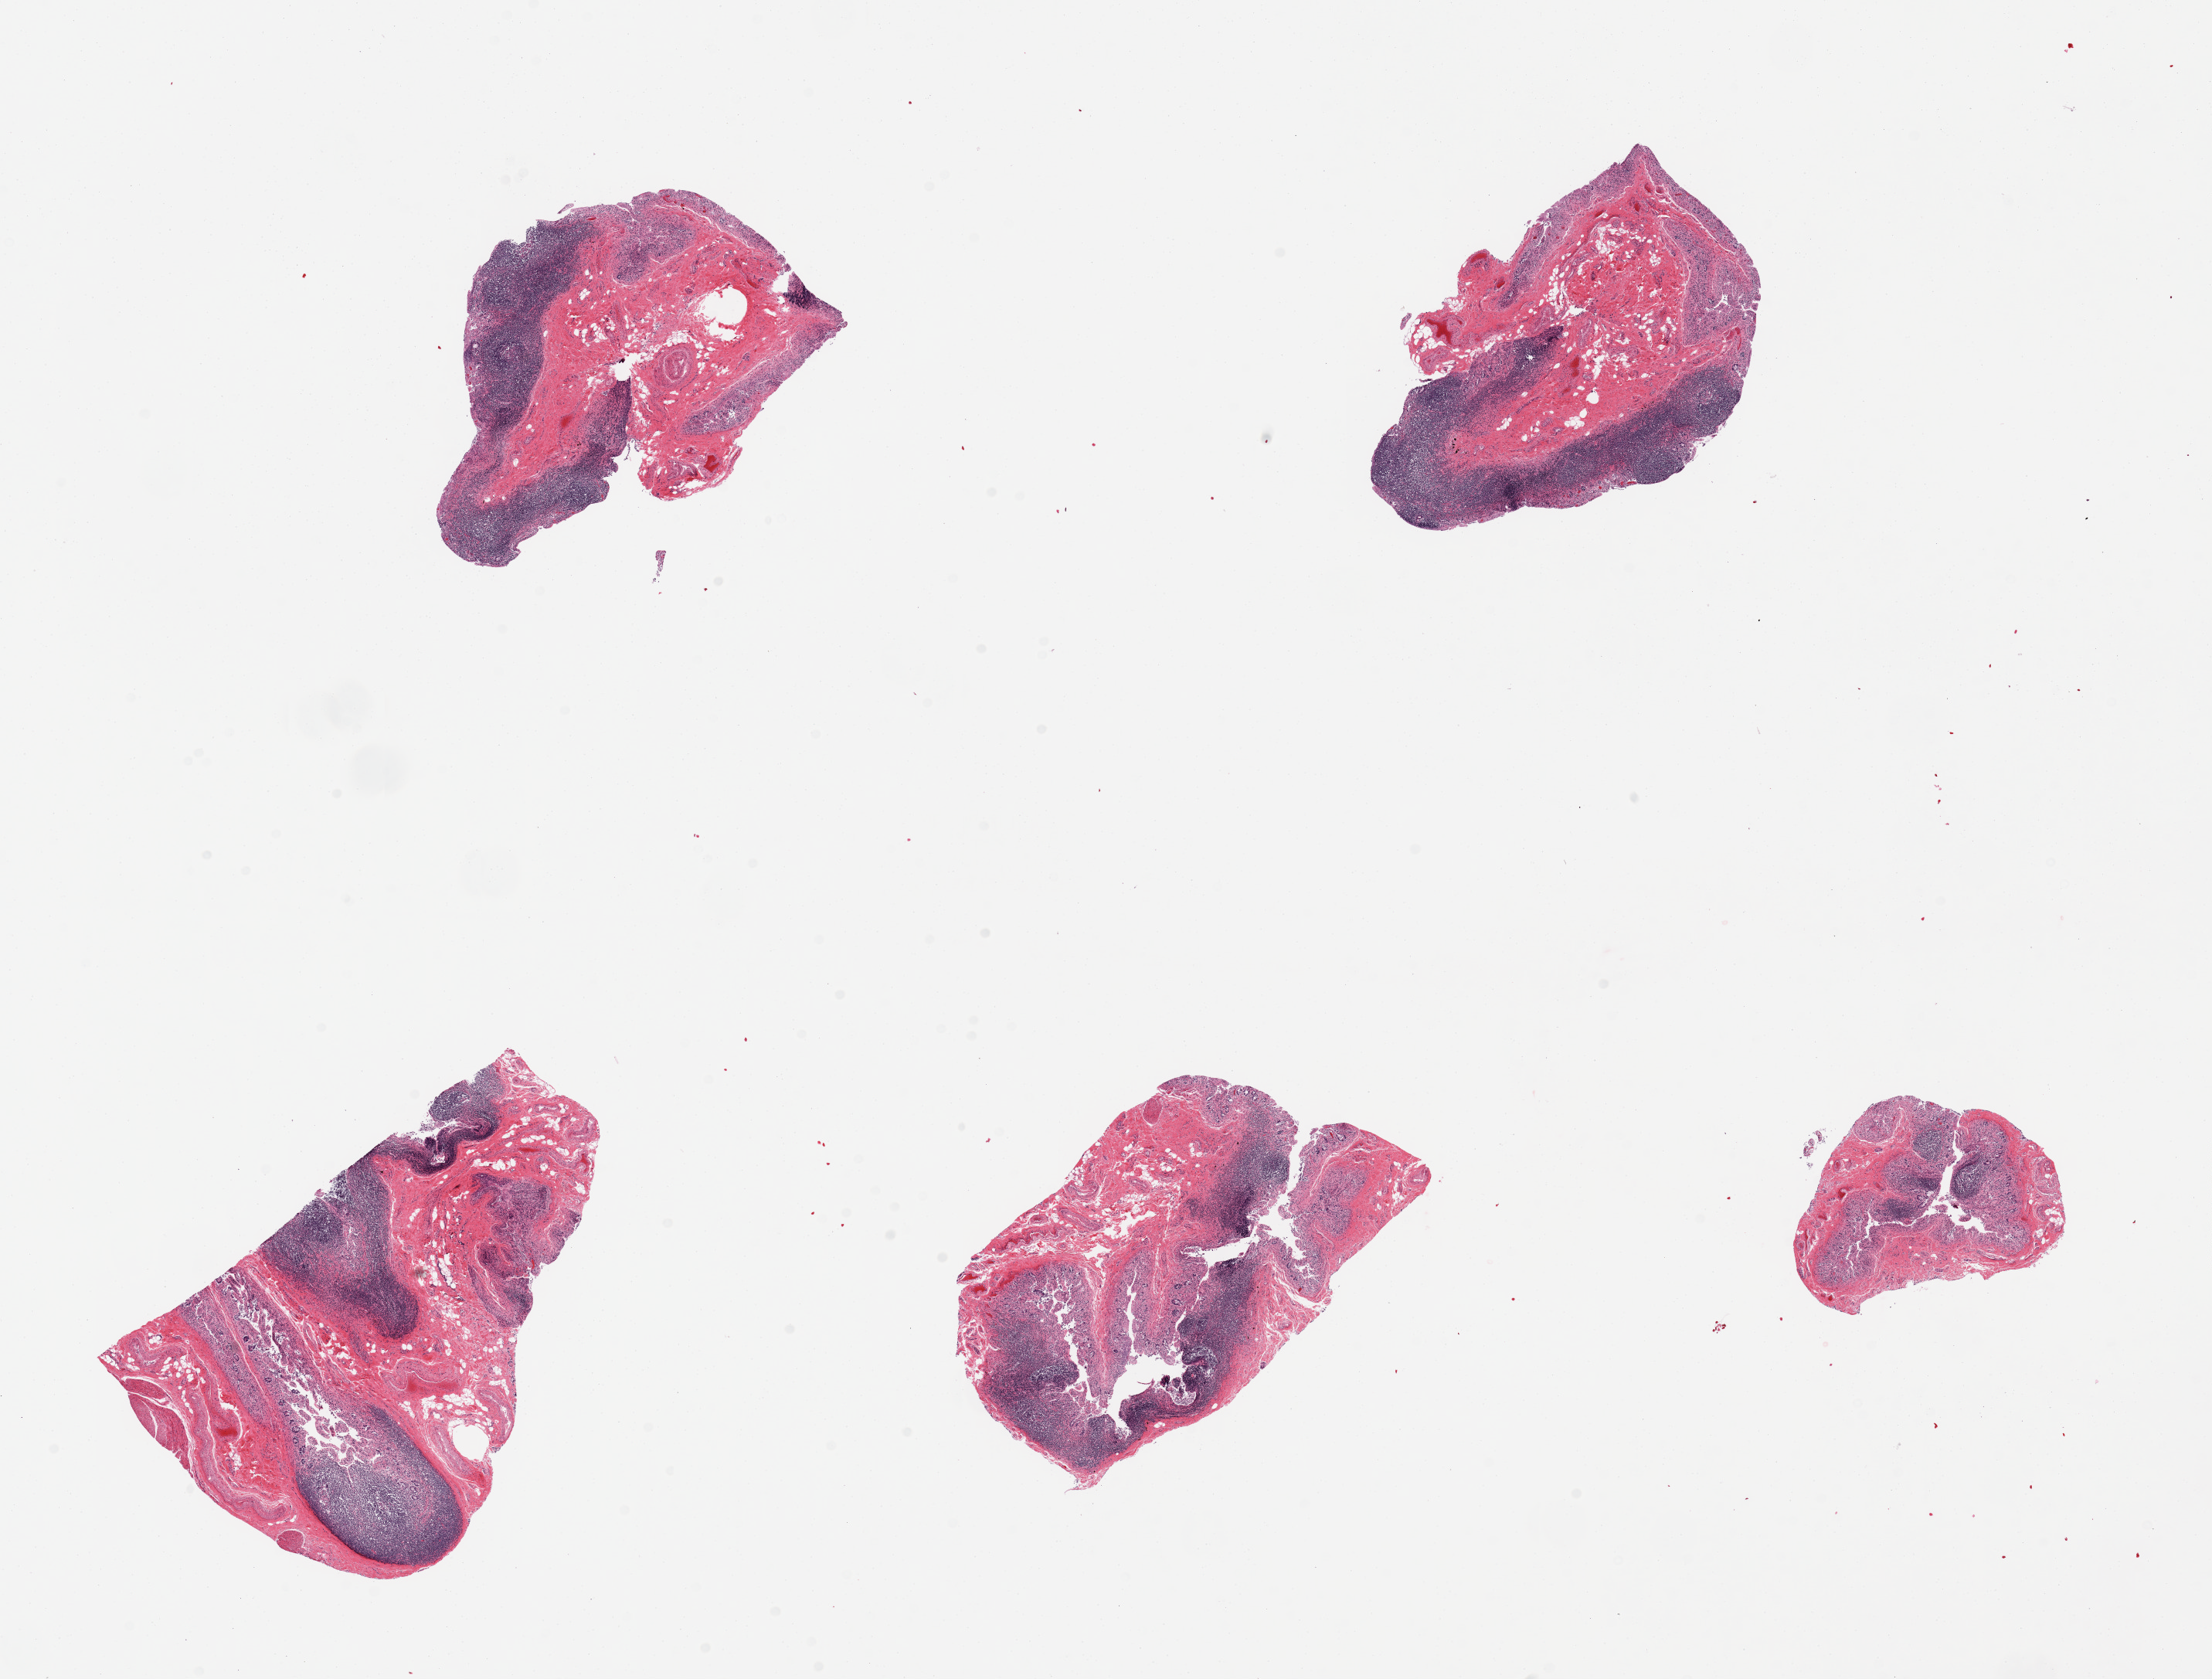
Digitized haematoxylin and eosin-stained section, brightfield — shown as a low-resolution overview of the whole scanned area (about 22.6 x 17.2 mm, from a 20x scan). PAXgene-fixed, paraffin-embedded tissue. Sampled site (target tissue): ileum. Donor tissue sample. Donor: female.
Pathologist's review note for this sample: 5 pieces; abundant lymphoid tissue; mucosa autolyzed but lymphoid tissue still appears intact.